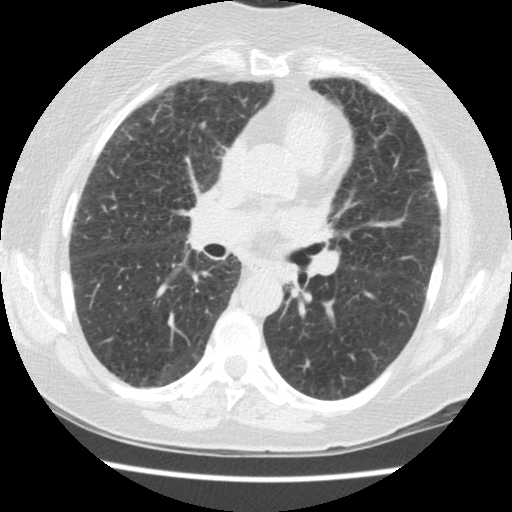
Chest CT (low-dose screening protocol), one axial image. Second screening round (one year after baseline). Lung window (W 1500 / L -600 HU). 512 × 512 image matrix. Female, age 60 years at enrolment. Former smoker at enrolment.
Lesion marked by an expert reader, bounding box [x1, y1, x2, y2] px = [268, 257, 315, 302]. The exam's reader record, not a measurement of the box and not confirmed to be the same lesion: non-calcified nodule or mass ≥4 mm, left lower lobe, 5 × 4 mm, smooth margins, soft tissue attenuation, pre-existing on the prior screen: yes; interval growth: no. Lung cancer was diagnosed 423 days after this screen: small cell carcinoma, NOS, left lower lobe, undifferentiated (G4), stage IV (AJCC 6th edition), 69 mm at pathology.